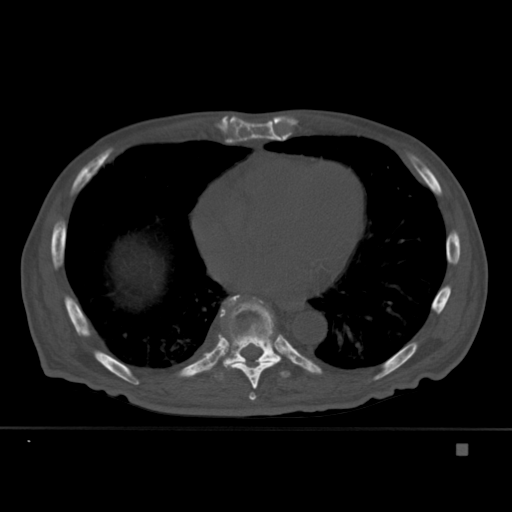
CT including the spine, one axial slice; position 256 of 451 along the scan axis; bone window (W 1800 / L 400 HU); 512 × 512 image matrix. Patient: male, 75 years. From the clinical record (not read from this slice): primary cancer: prostate.
Structures marked on this image (semi-automatic segmentation, software-assisted and operator-edited):
- T7 vertebra: bounding box <249,392,257,401> (left, top, right, bottom; pixels)
- T8 vertebra: <224,299,274,389>
- T9 vertebra: <206,295,290,380>